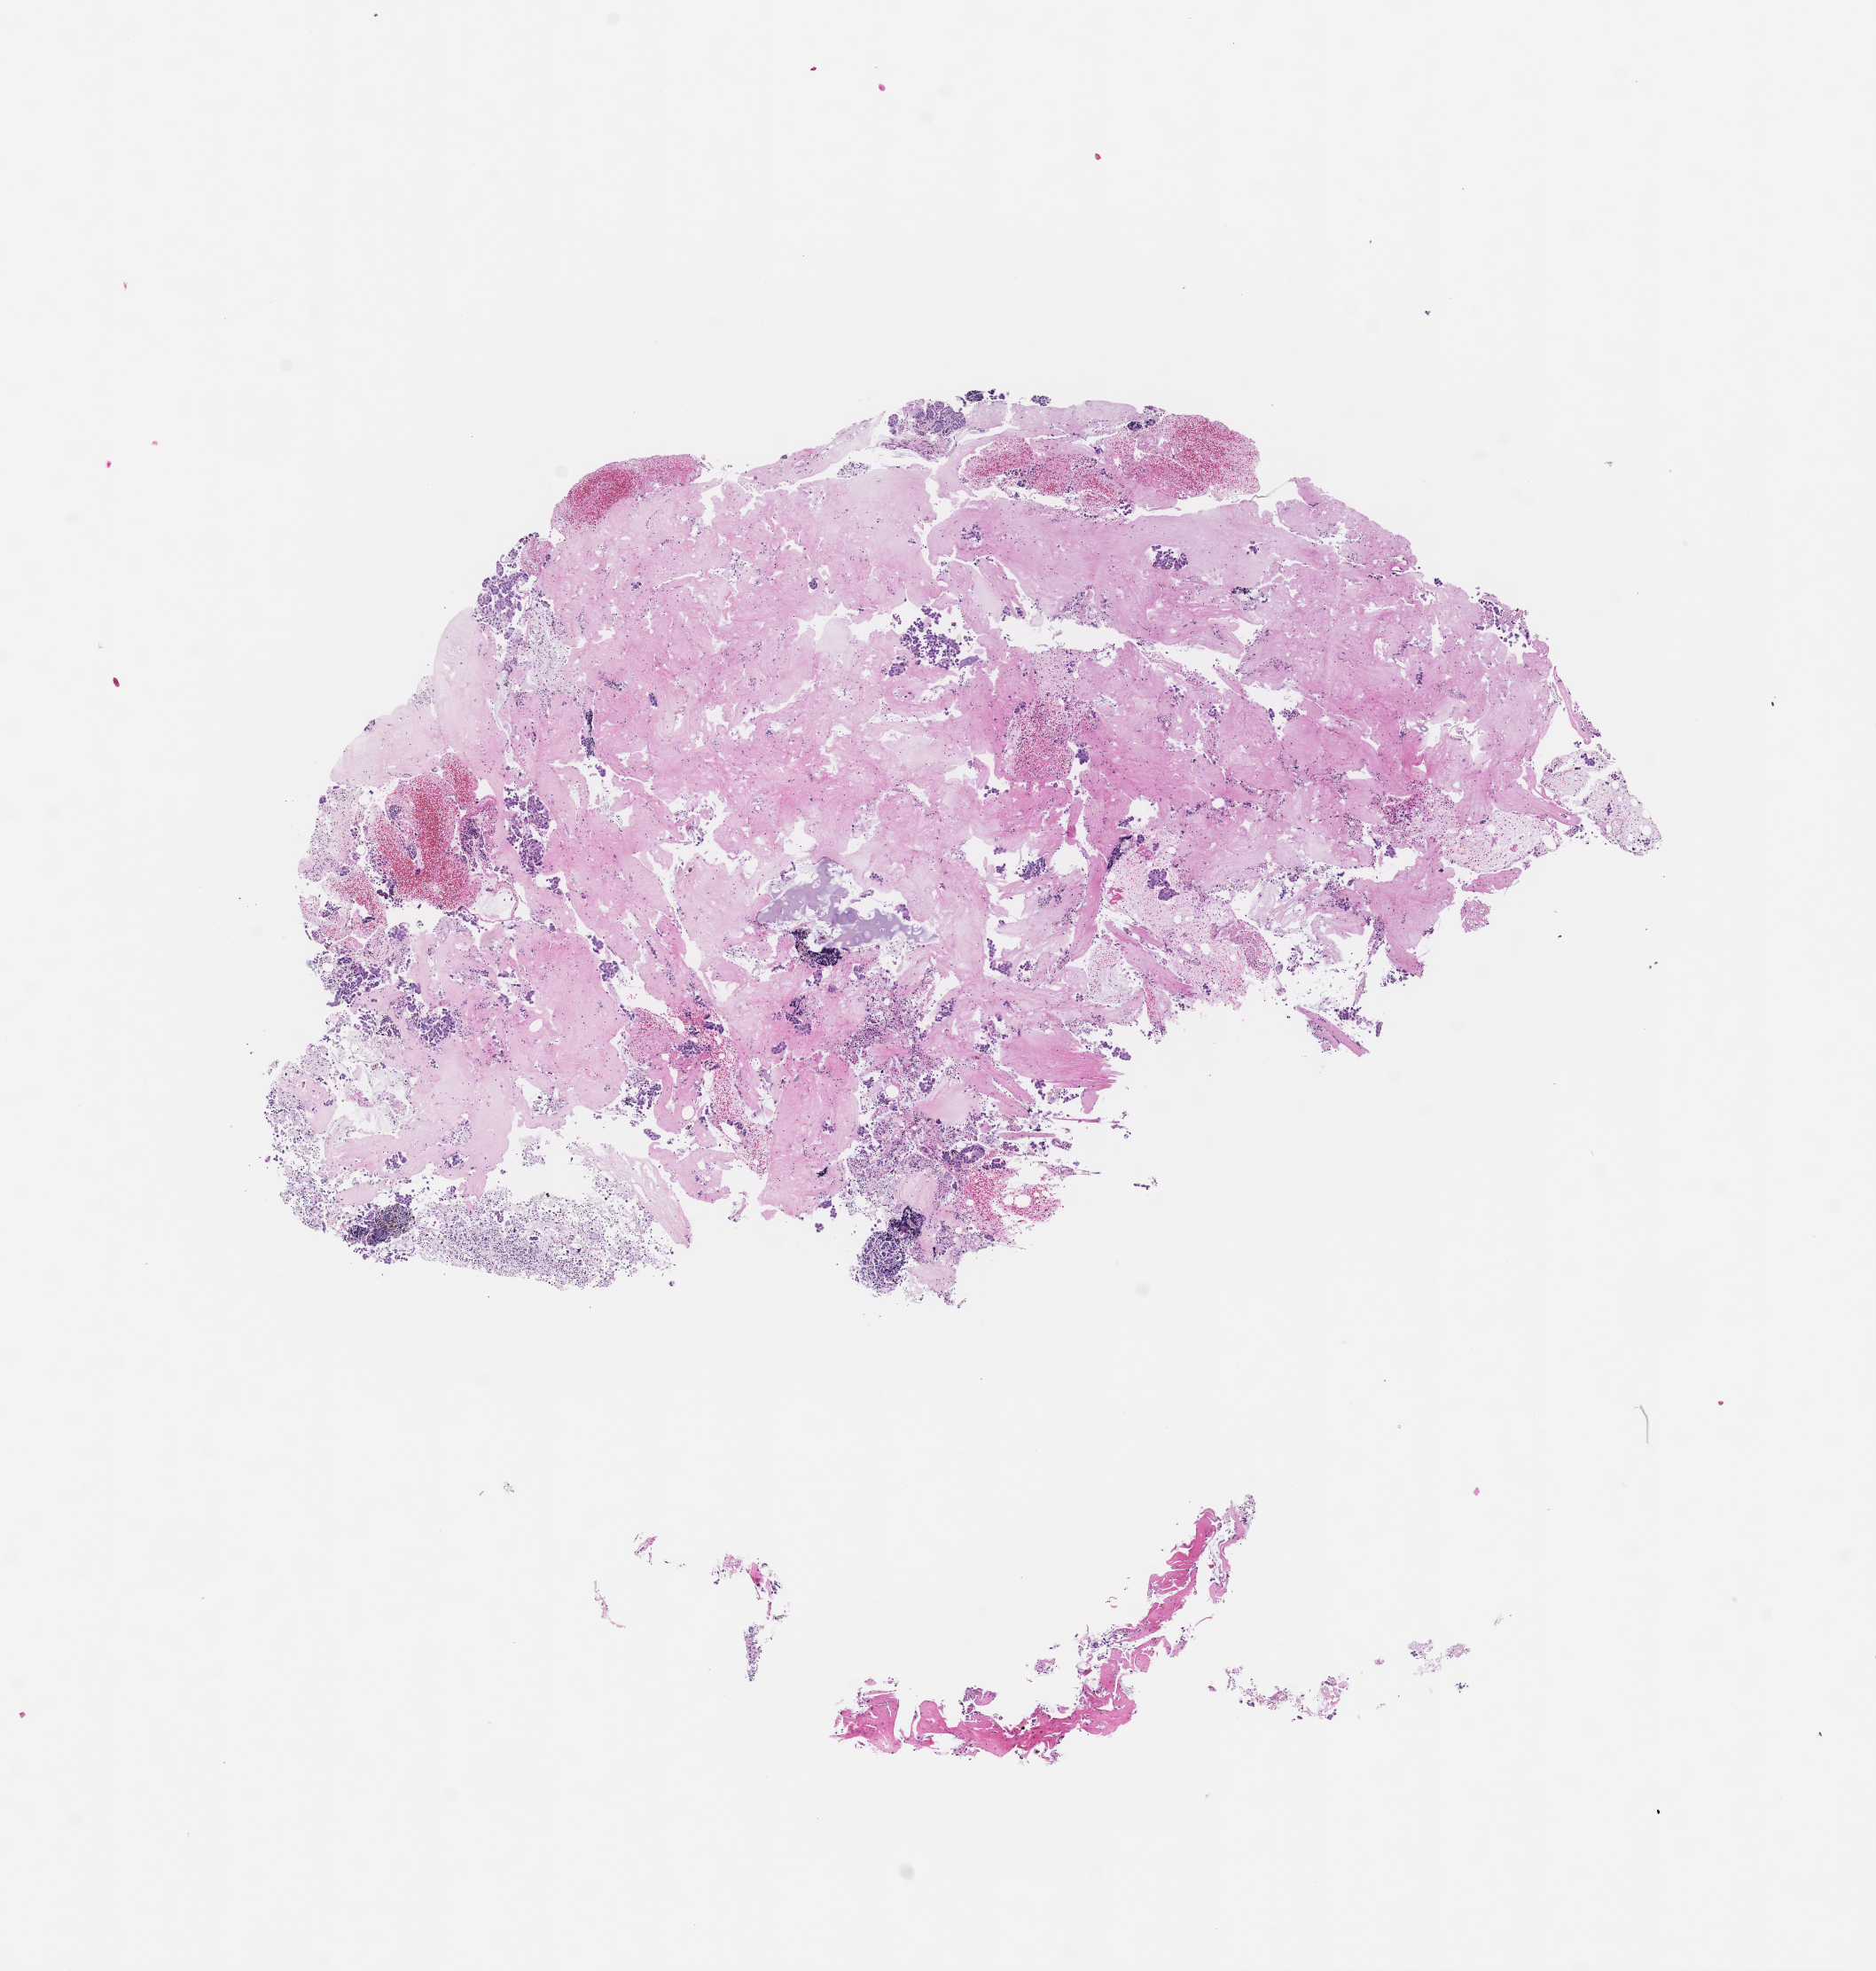
Haematoxylin and eosin whole-slide image, a low-resolution overview of the entire scanned area, about 8.5 x 9.0 mm, formalin-fixed paraffin-embedded section, archival tissue. Patient sex: male.
This section: metastasis (sampled organ not recorded). Primary diagnosis of the patient: Non-Small Cell Lung Carcinoma.